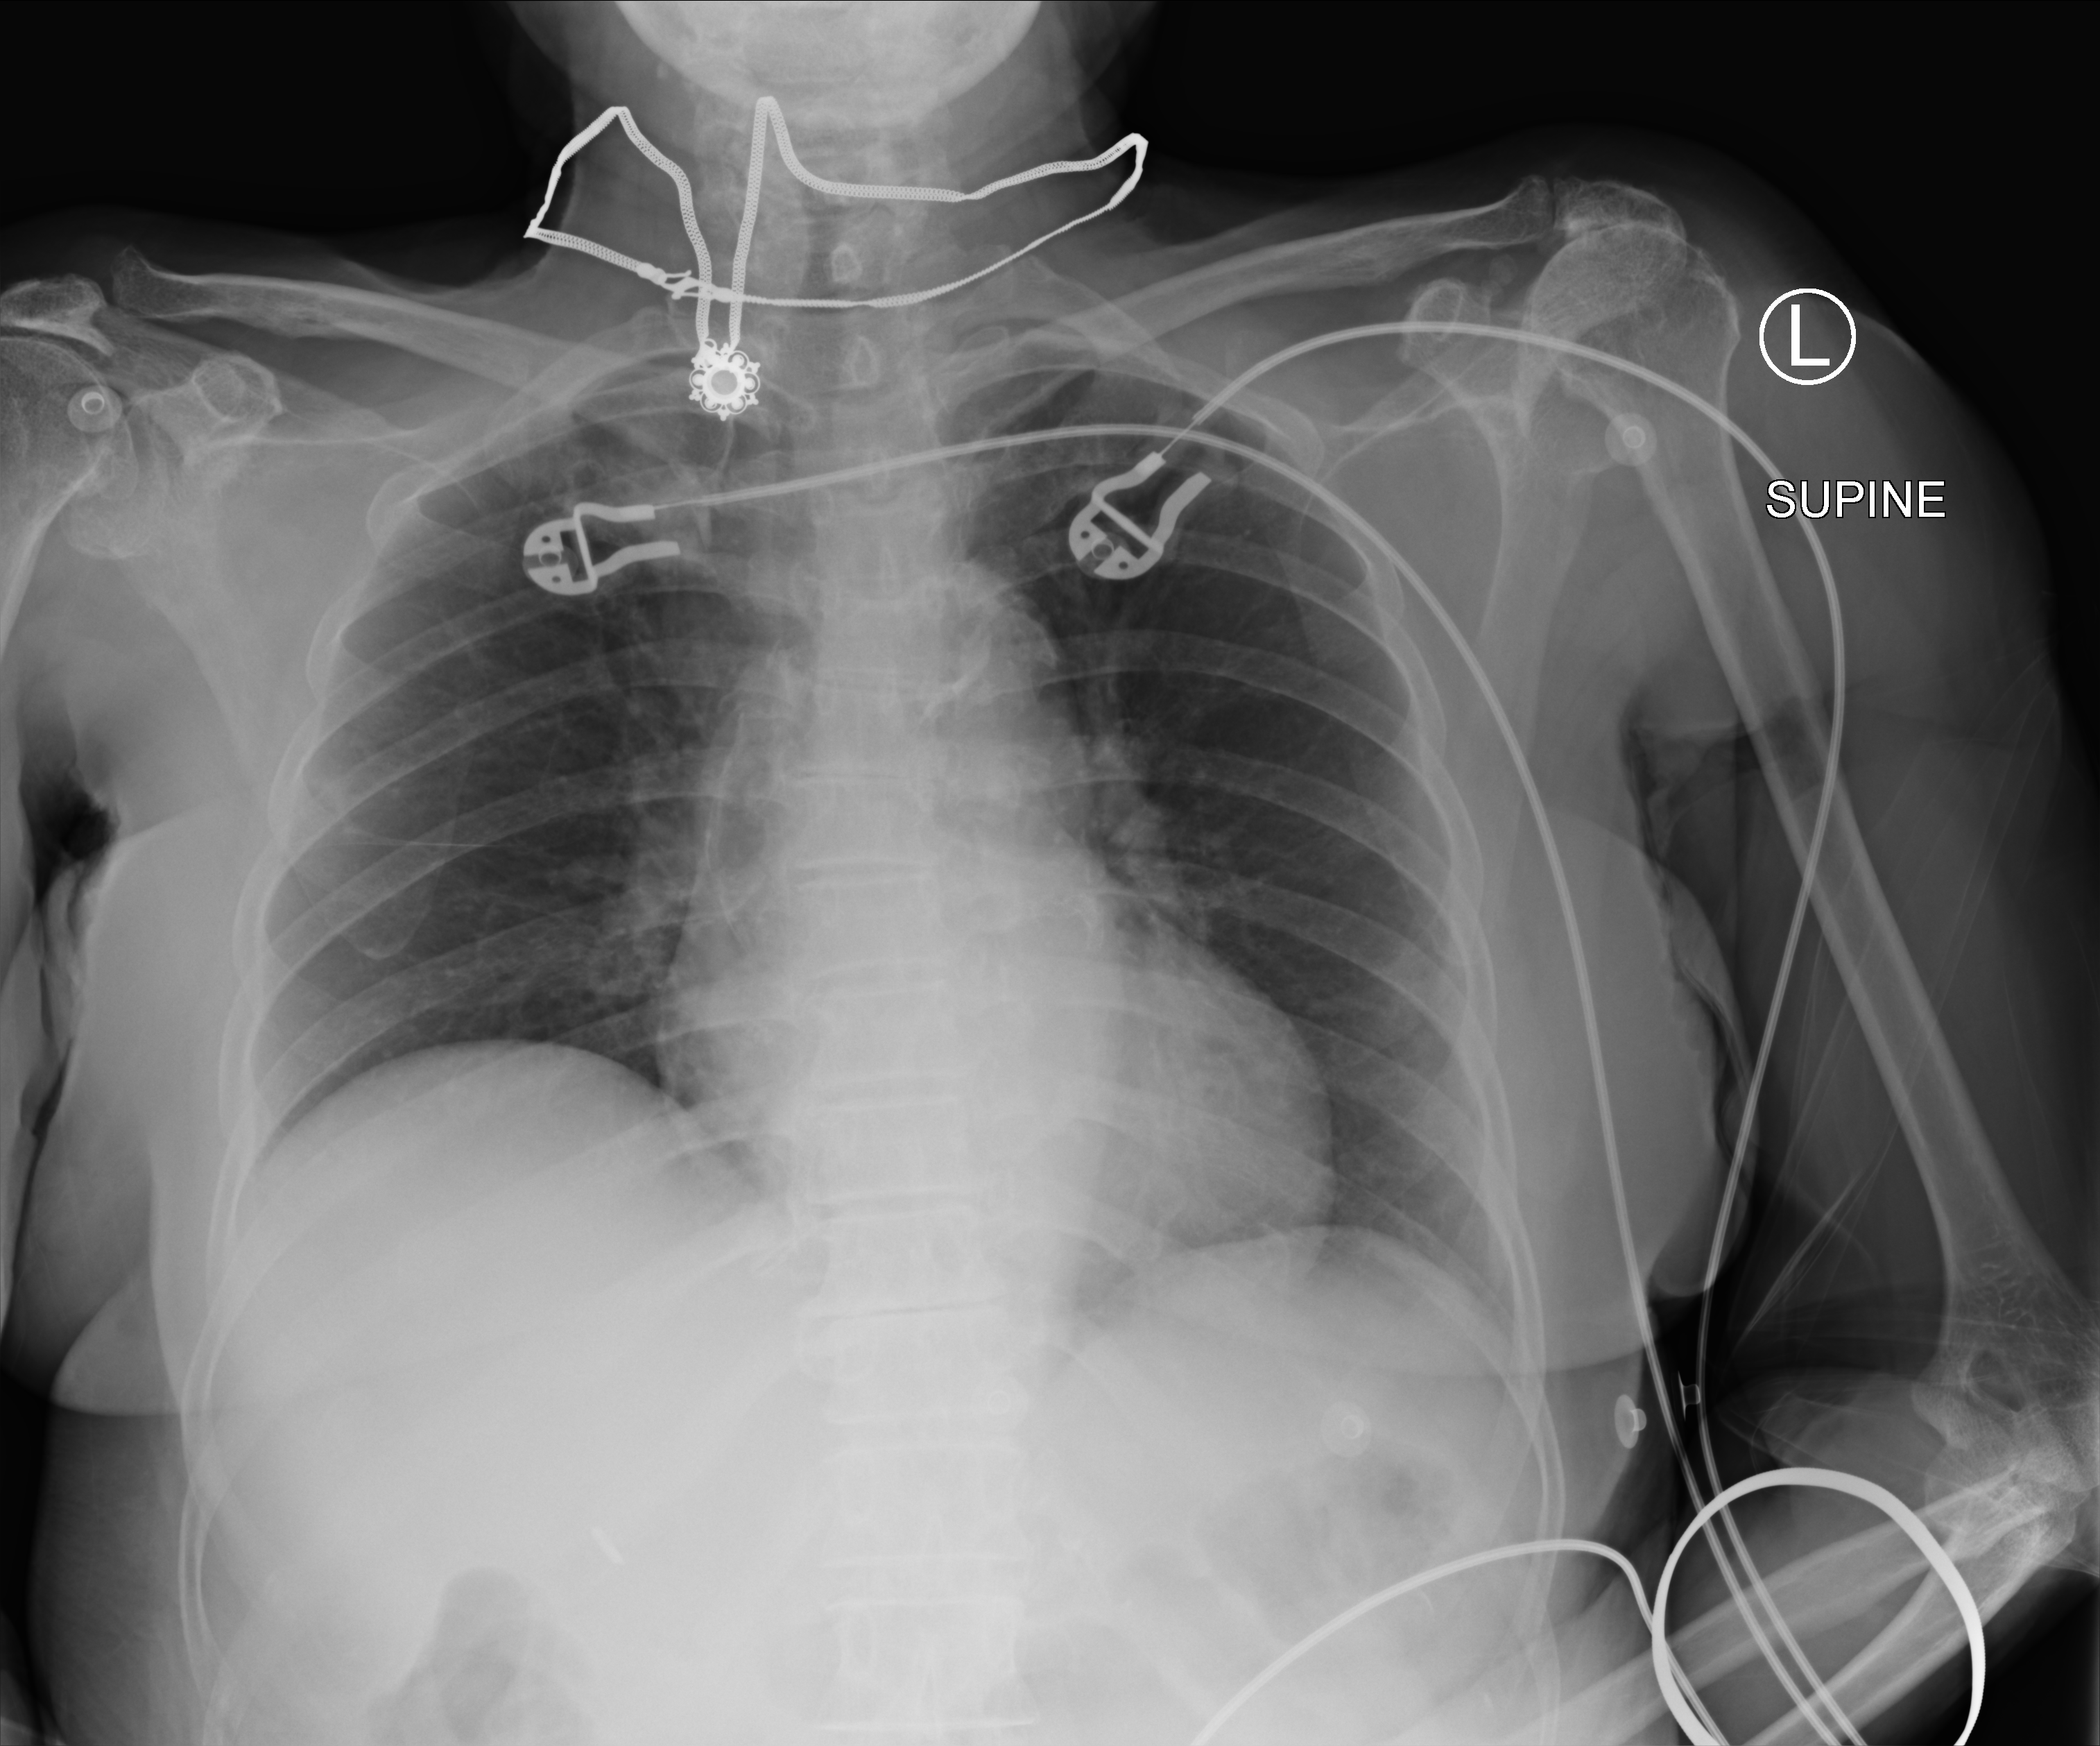
Chest X-ray (portable). Female patient hospitalised with COVID-19, age 75–90 years.
From the hospital-stay record, not from the radiograph (when in the stay this image was taken is not recorded): mechanically ventilated during this hospital stay: no.